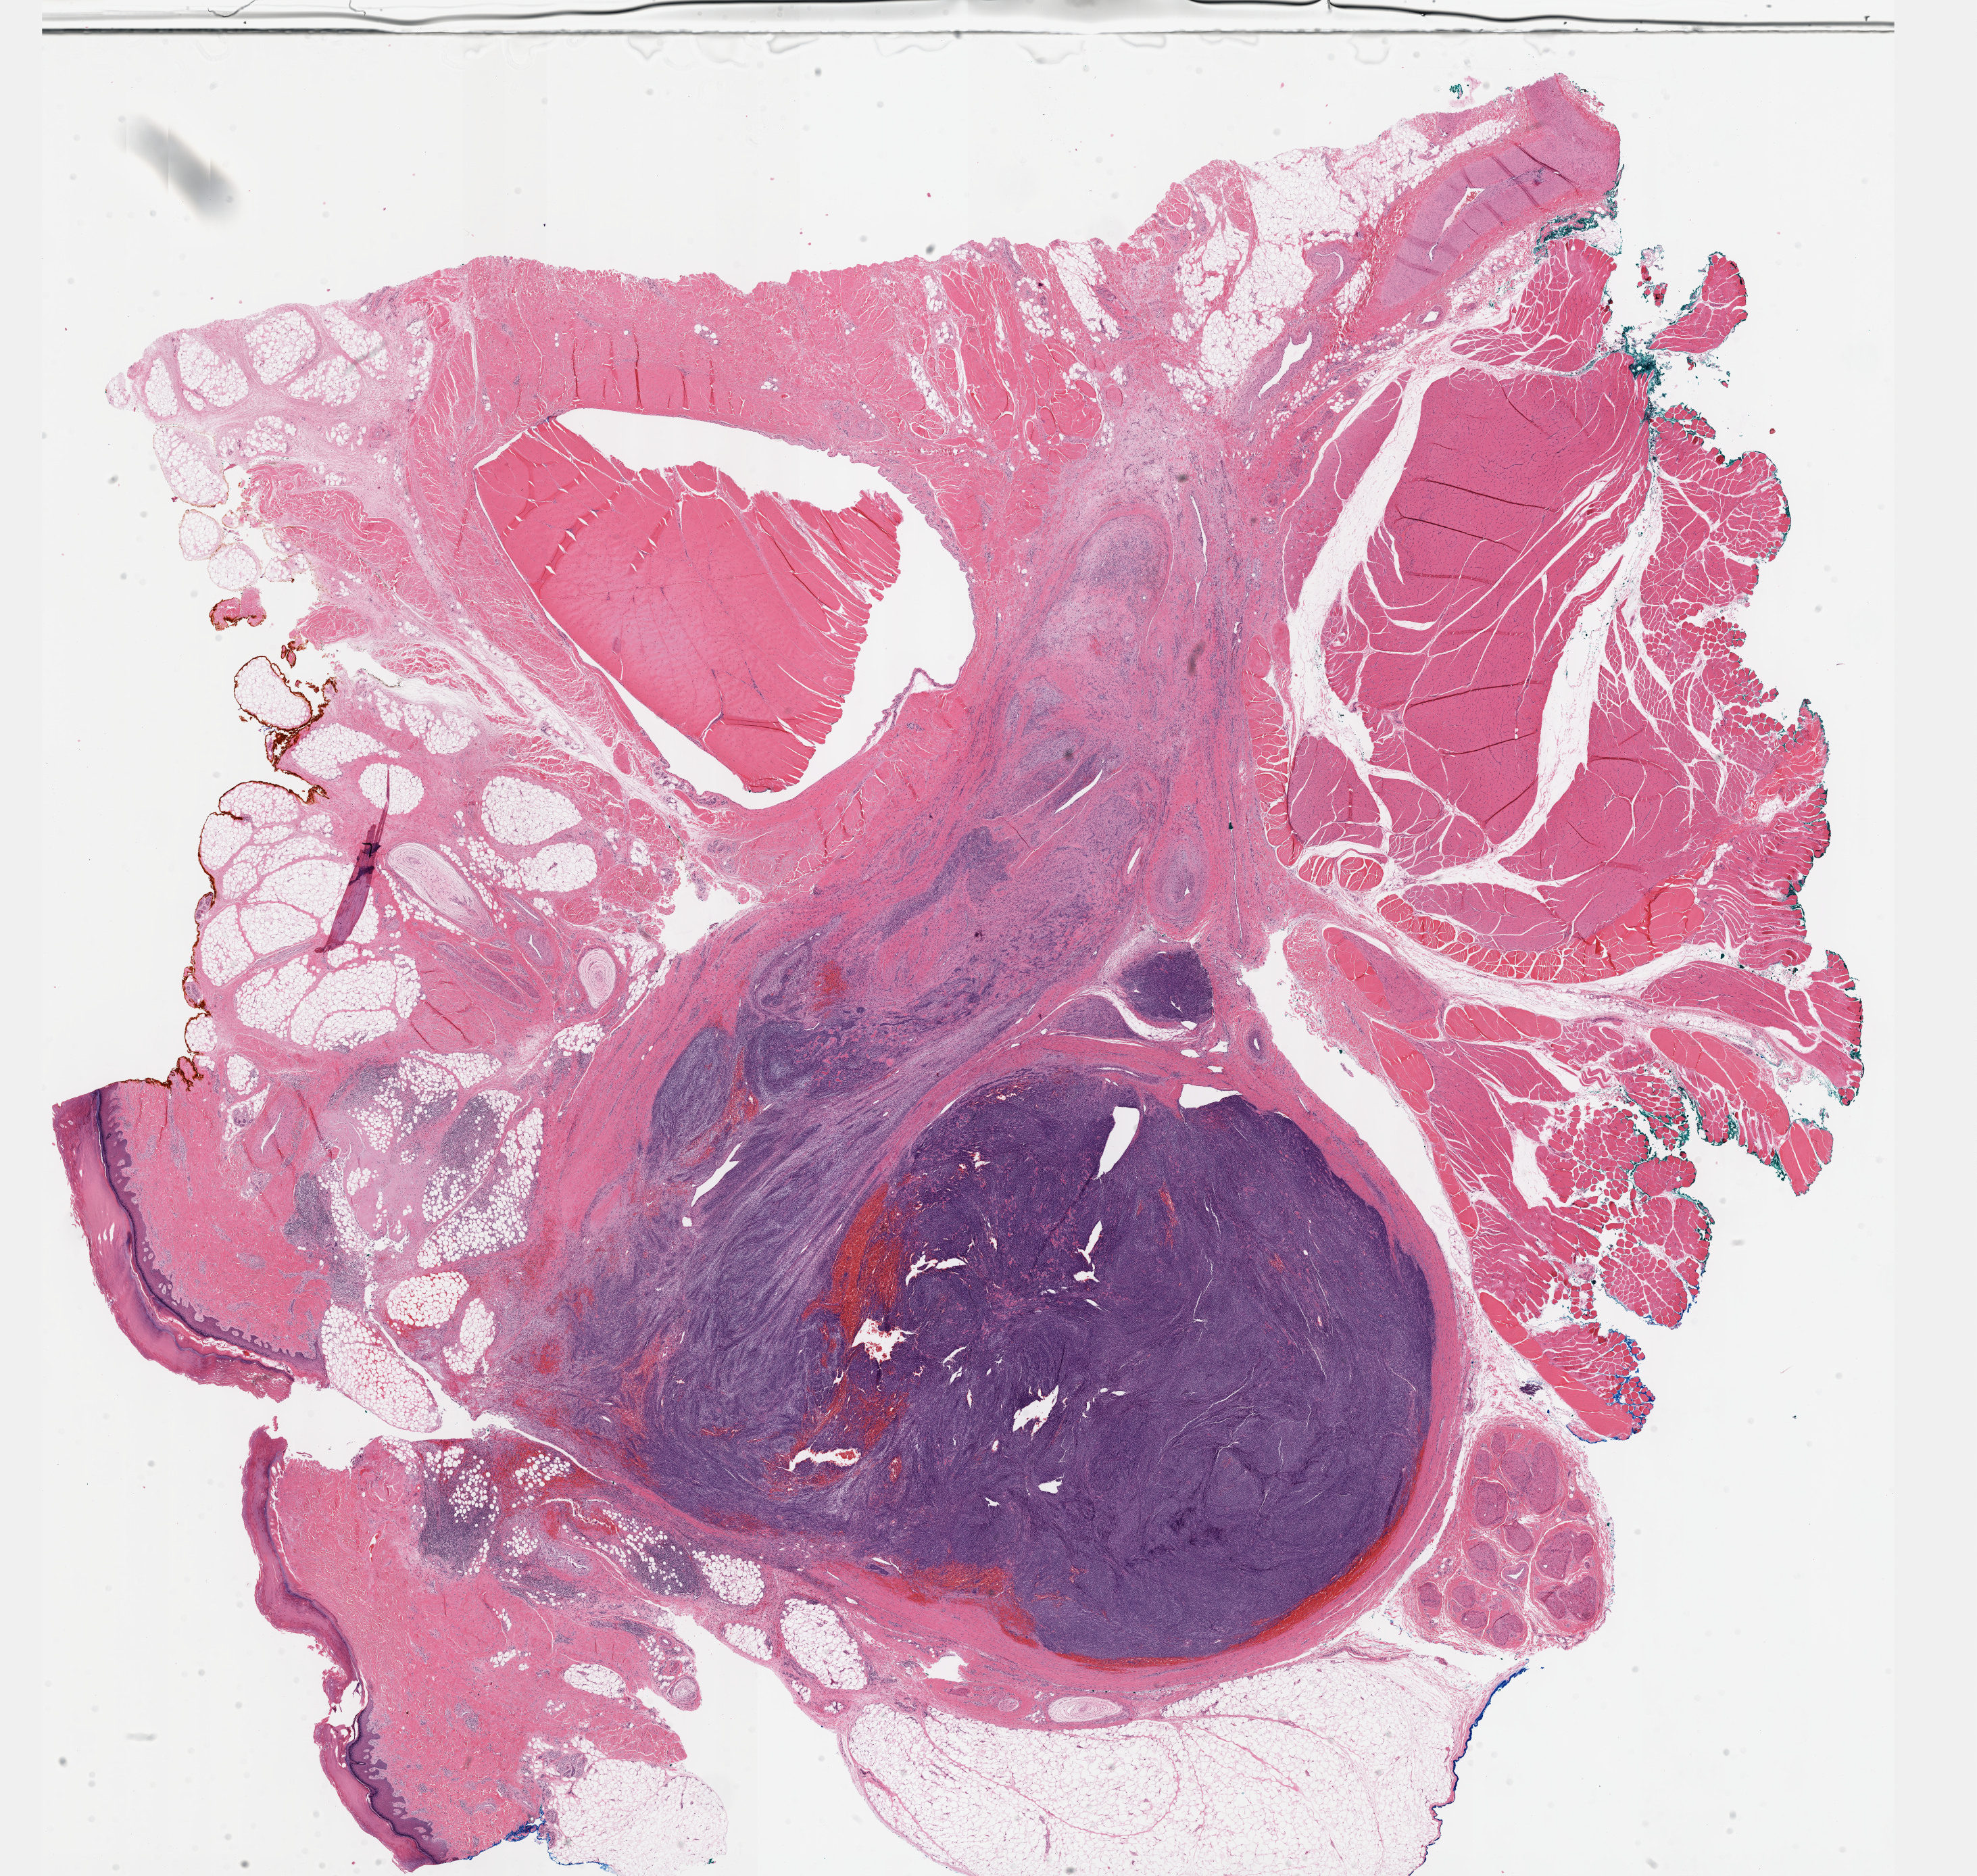
H&E whole-slide image — shown as a low-resolution overview of the whole scanned area (about 23.6 x 22.4 mm, acquisition: 40x scan); FFPE section; sample: primary tumour, connective, subcutaneous and other soft tissues. Patient: female, age at initial diagnosis 24 years.
• diagnosis: Synovial sarcoma, biphasic